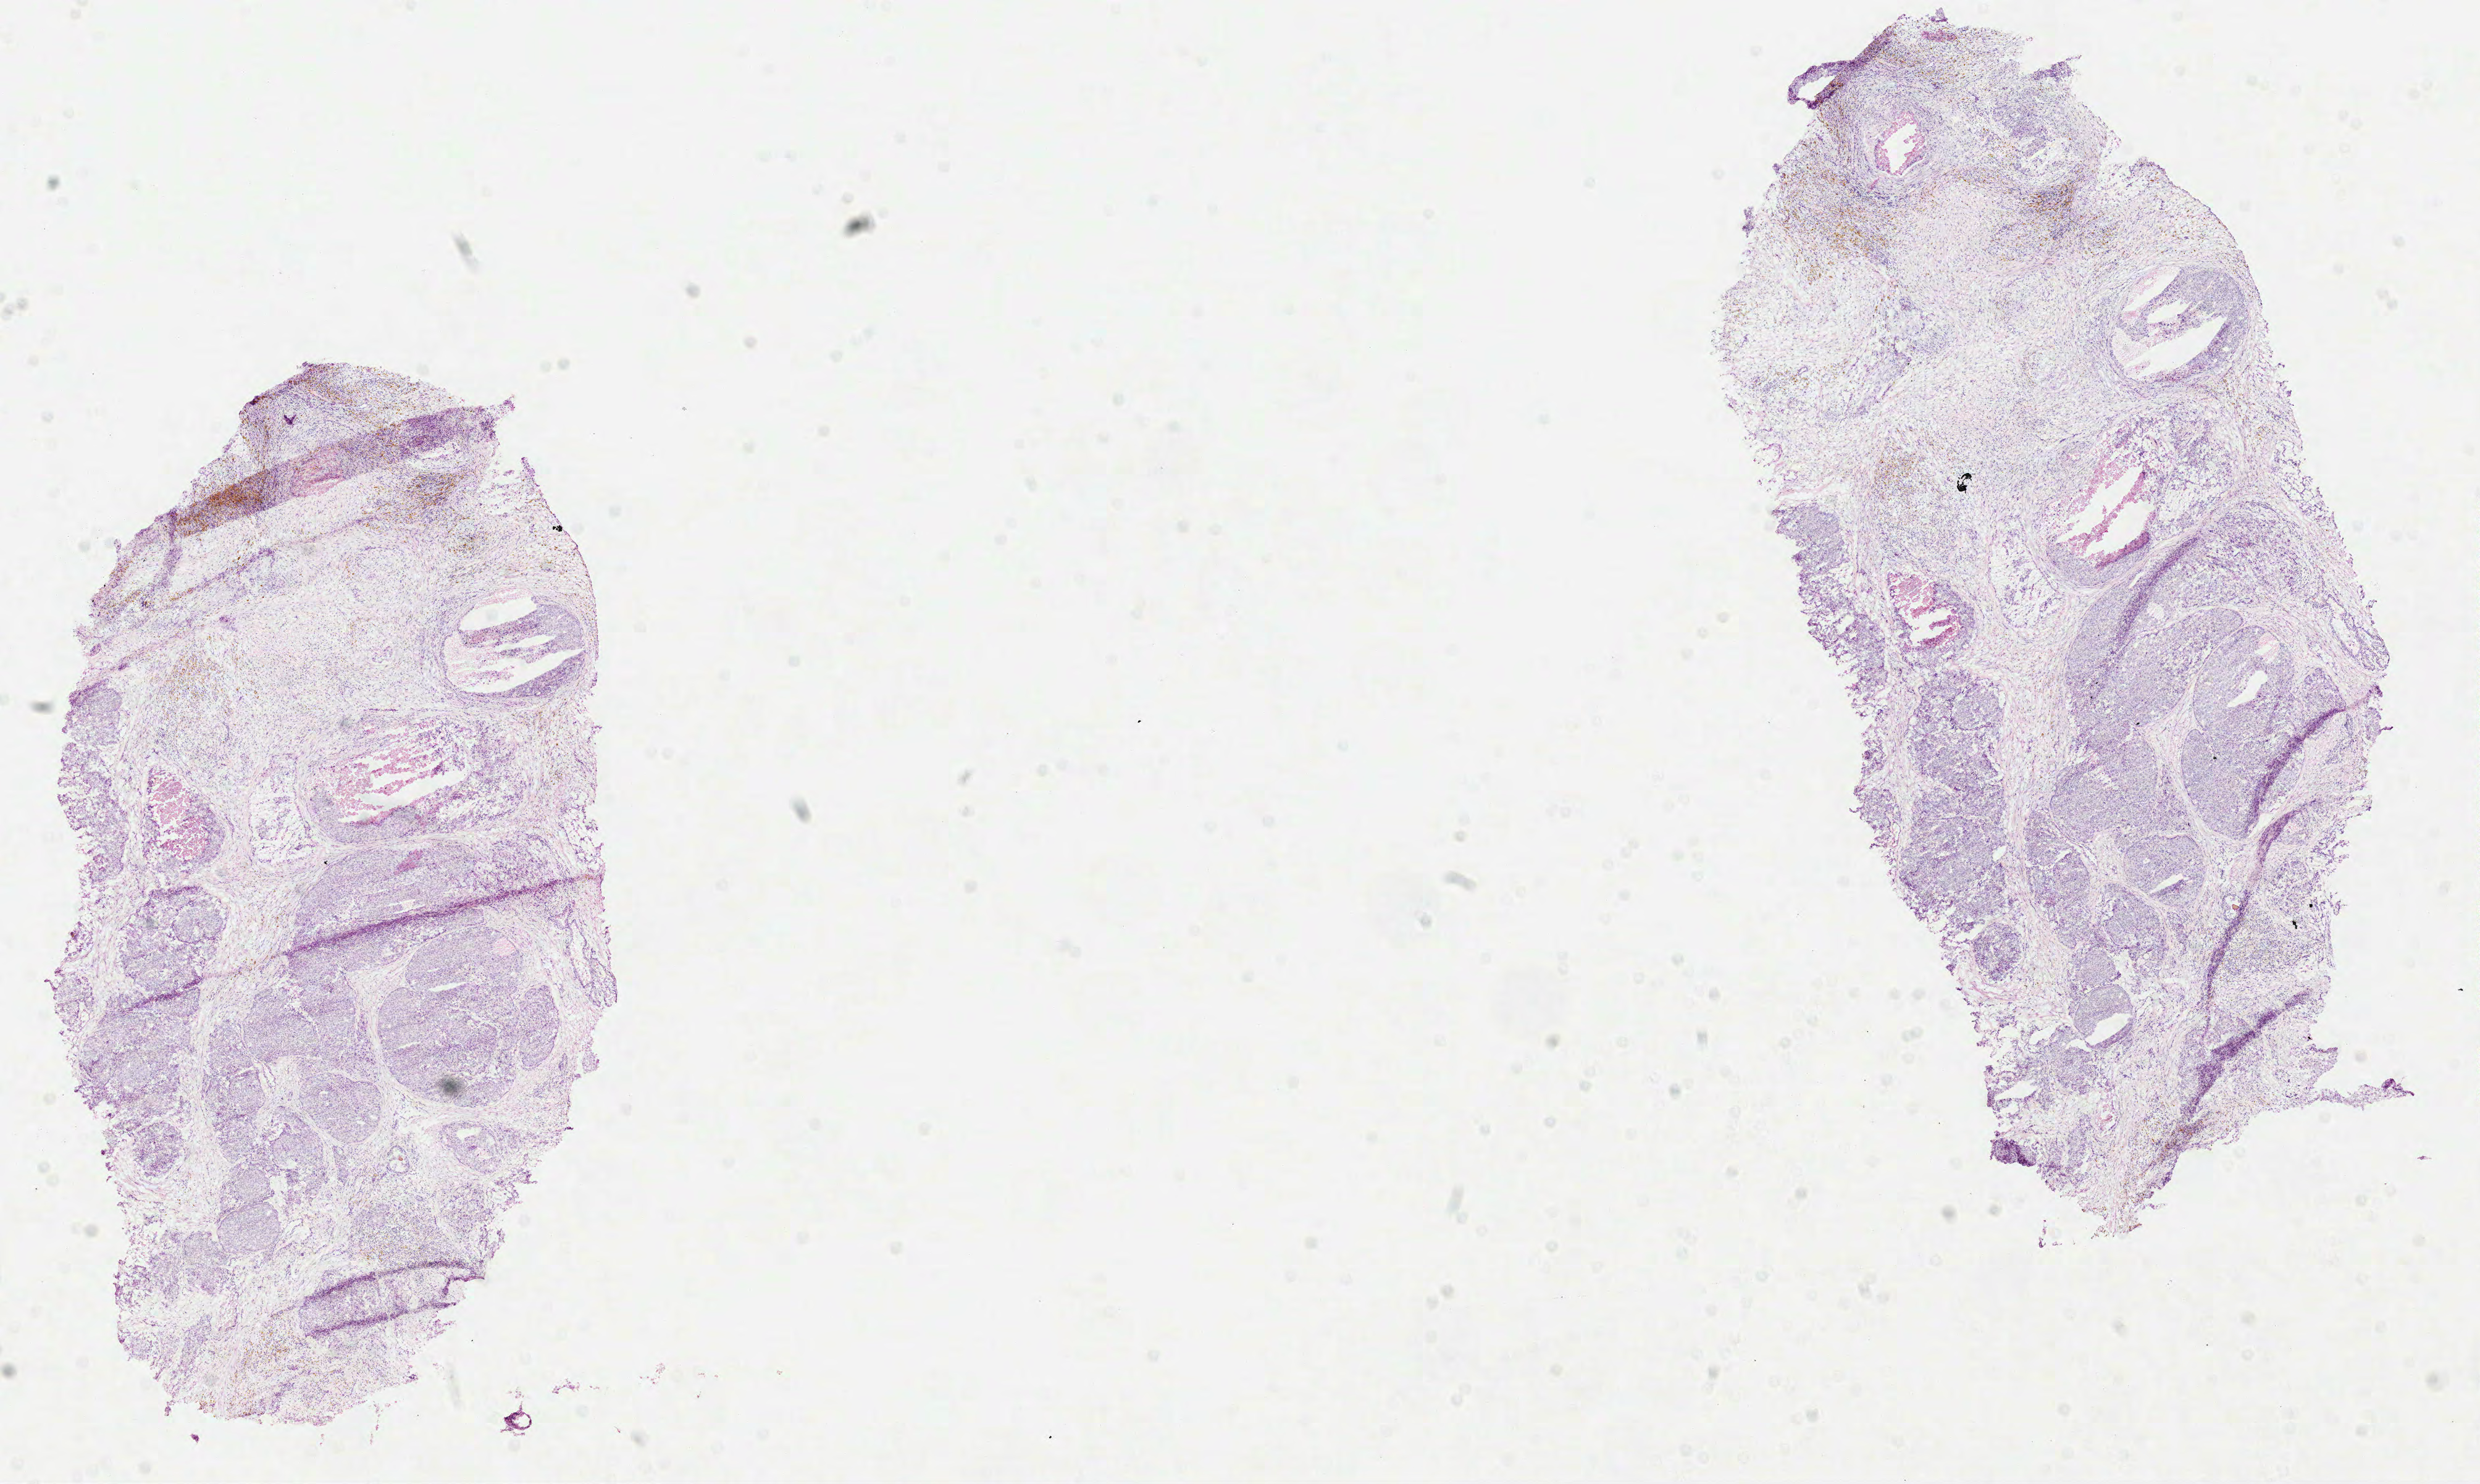
Whole-slide histology image, H&E — whole scanned area (about 16.2 x 9.7 mm) shown as a low-resolution overview; formalin-fixed paraffin-embedded (FFPE) diagnostic section; prostate, primary tumour sample. Male, age 65 years at initial diagnosis. Gleason score: 9 (4+5).
Pathologic diagnosis: Acinar cell carcinoma (prostate gland).